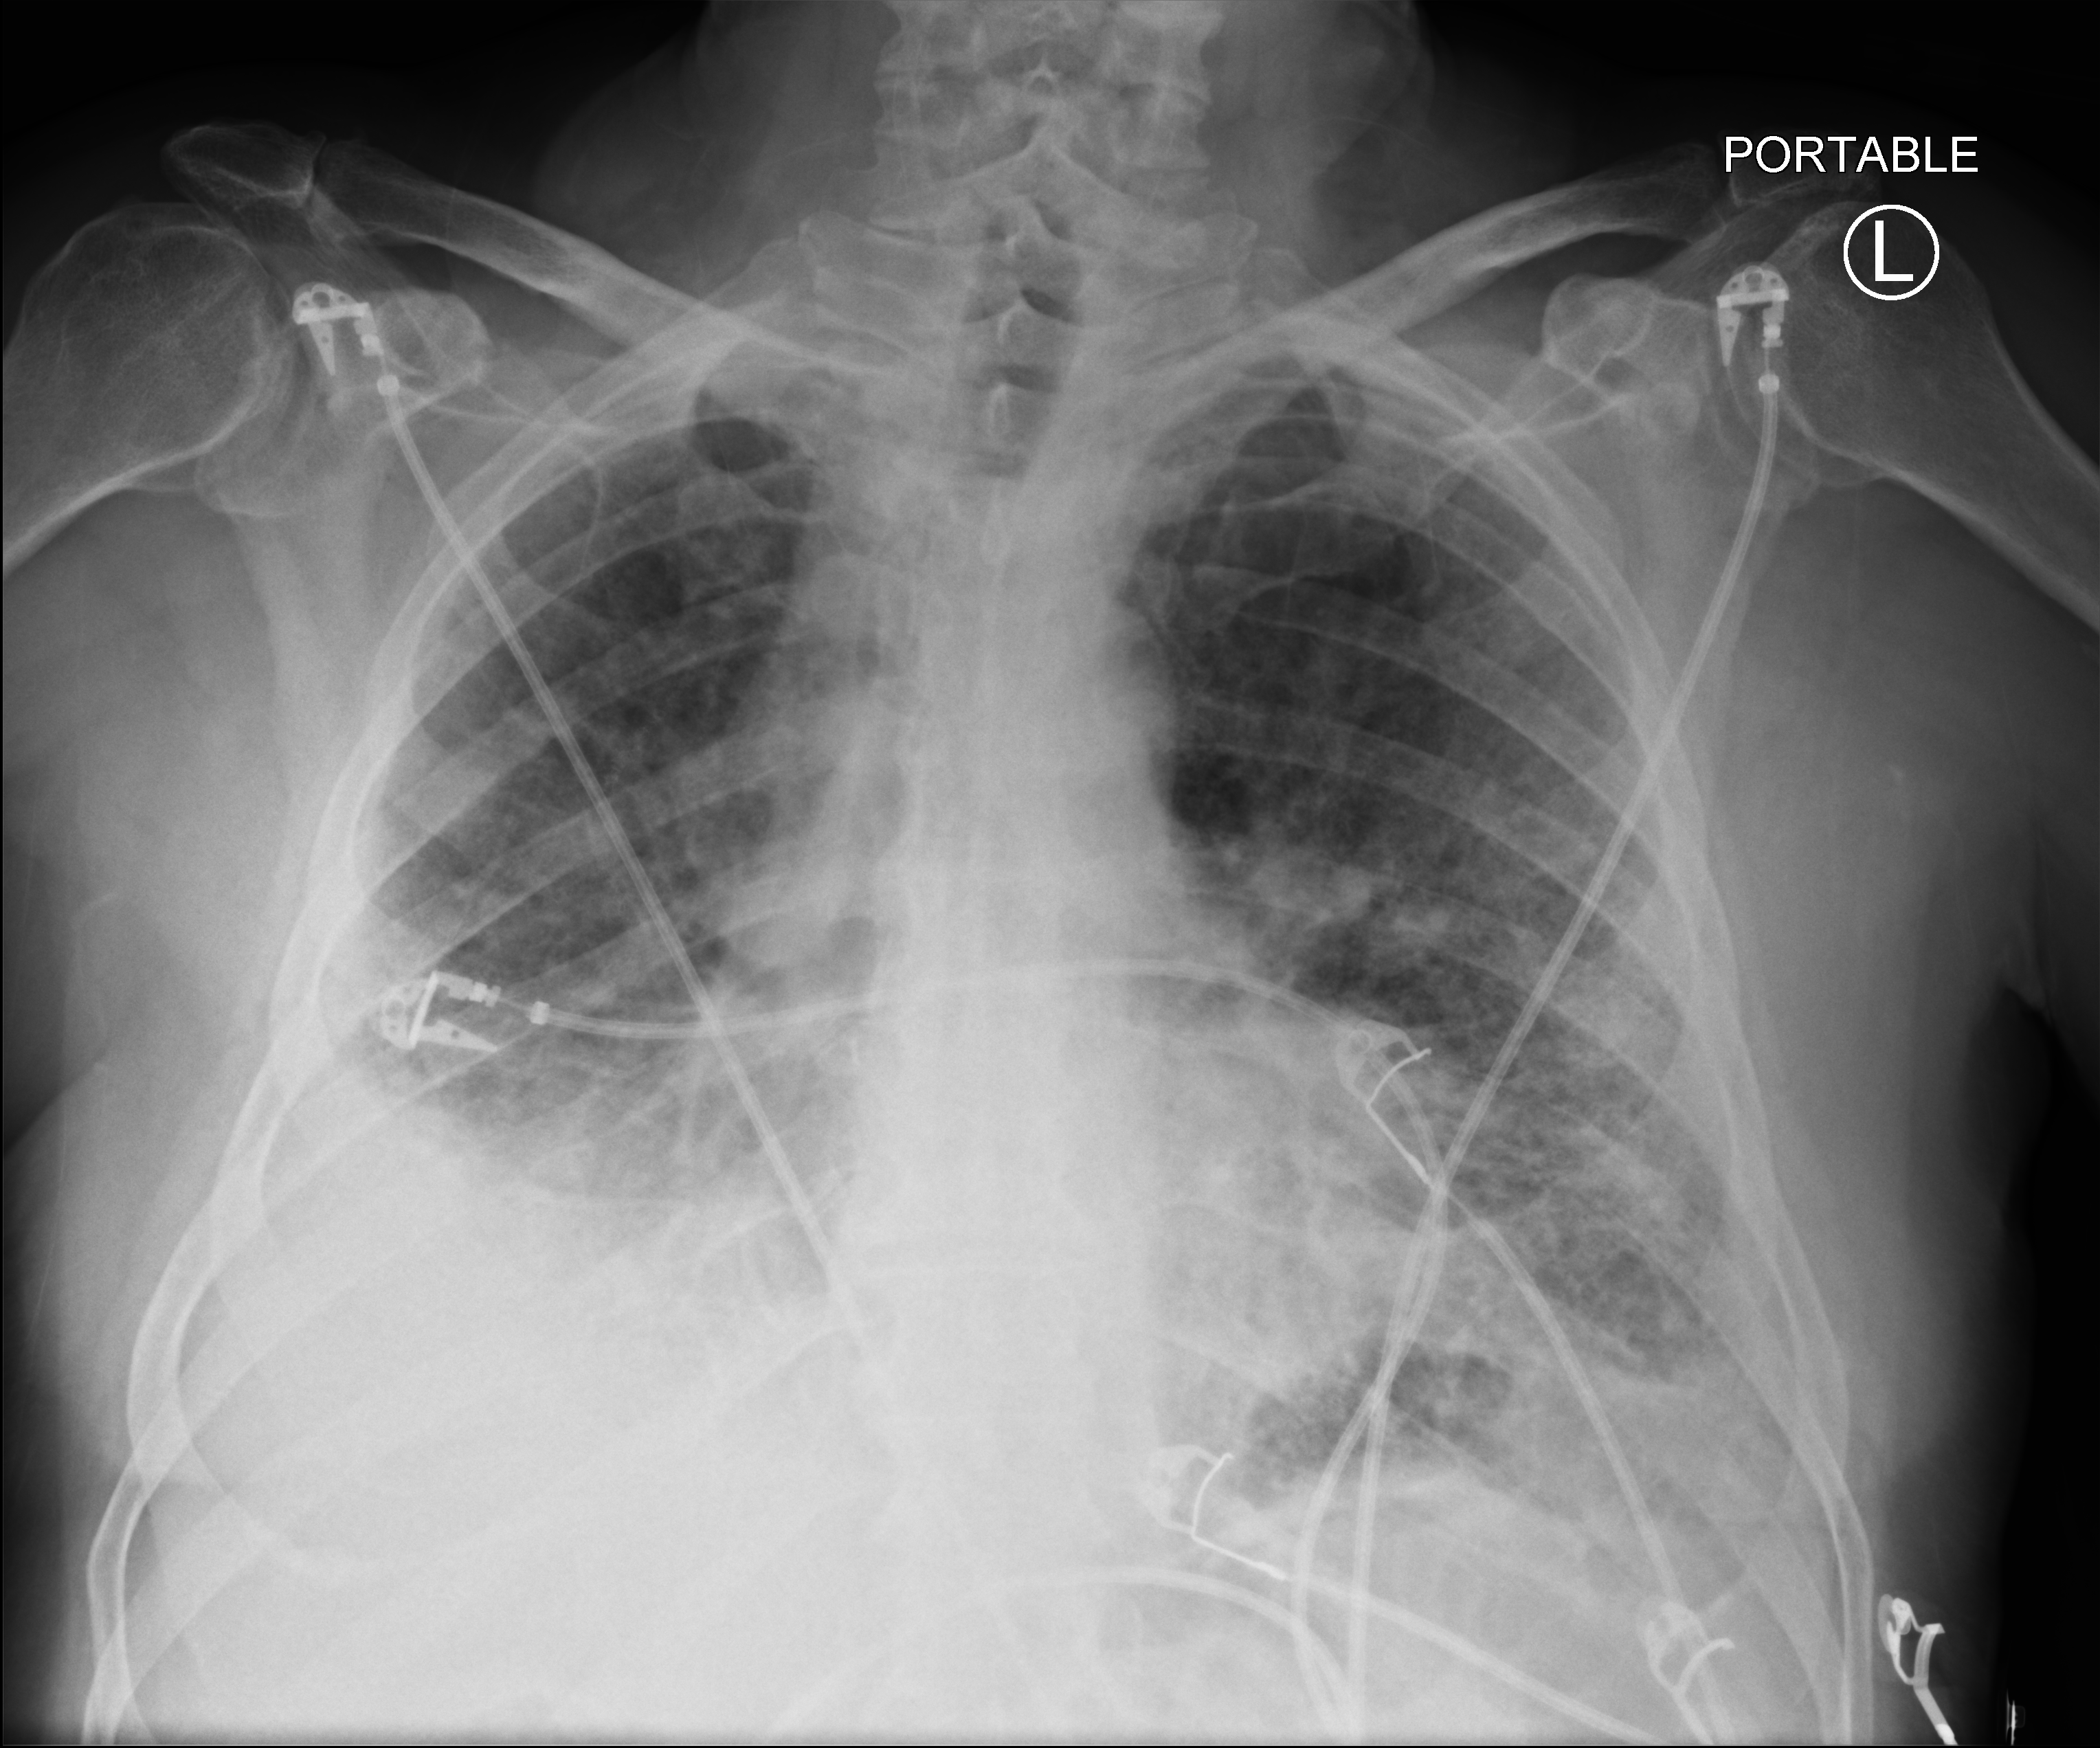
Chest X-ray (portable); anteroposterior (AP) projection. Patient hospitalised with COVID-19; male, aged 75–90 years.
Hospital-stay facts (about this admission, not read from this image; timing relative to this image not recorded):
- admitted to intensive care during this hospital stay: yes